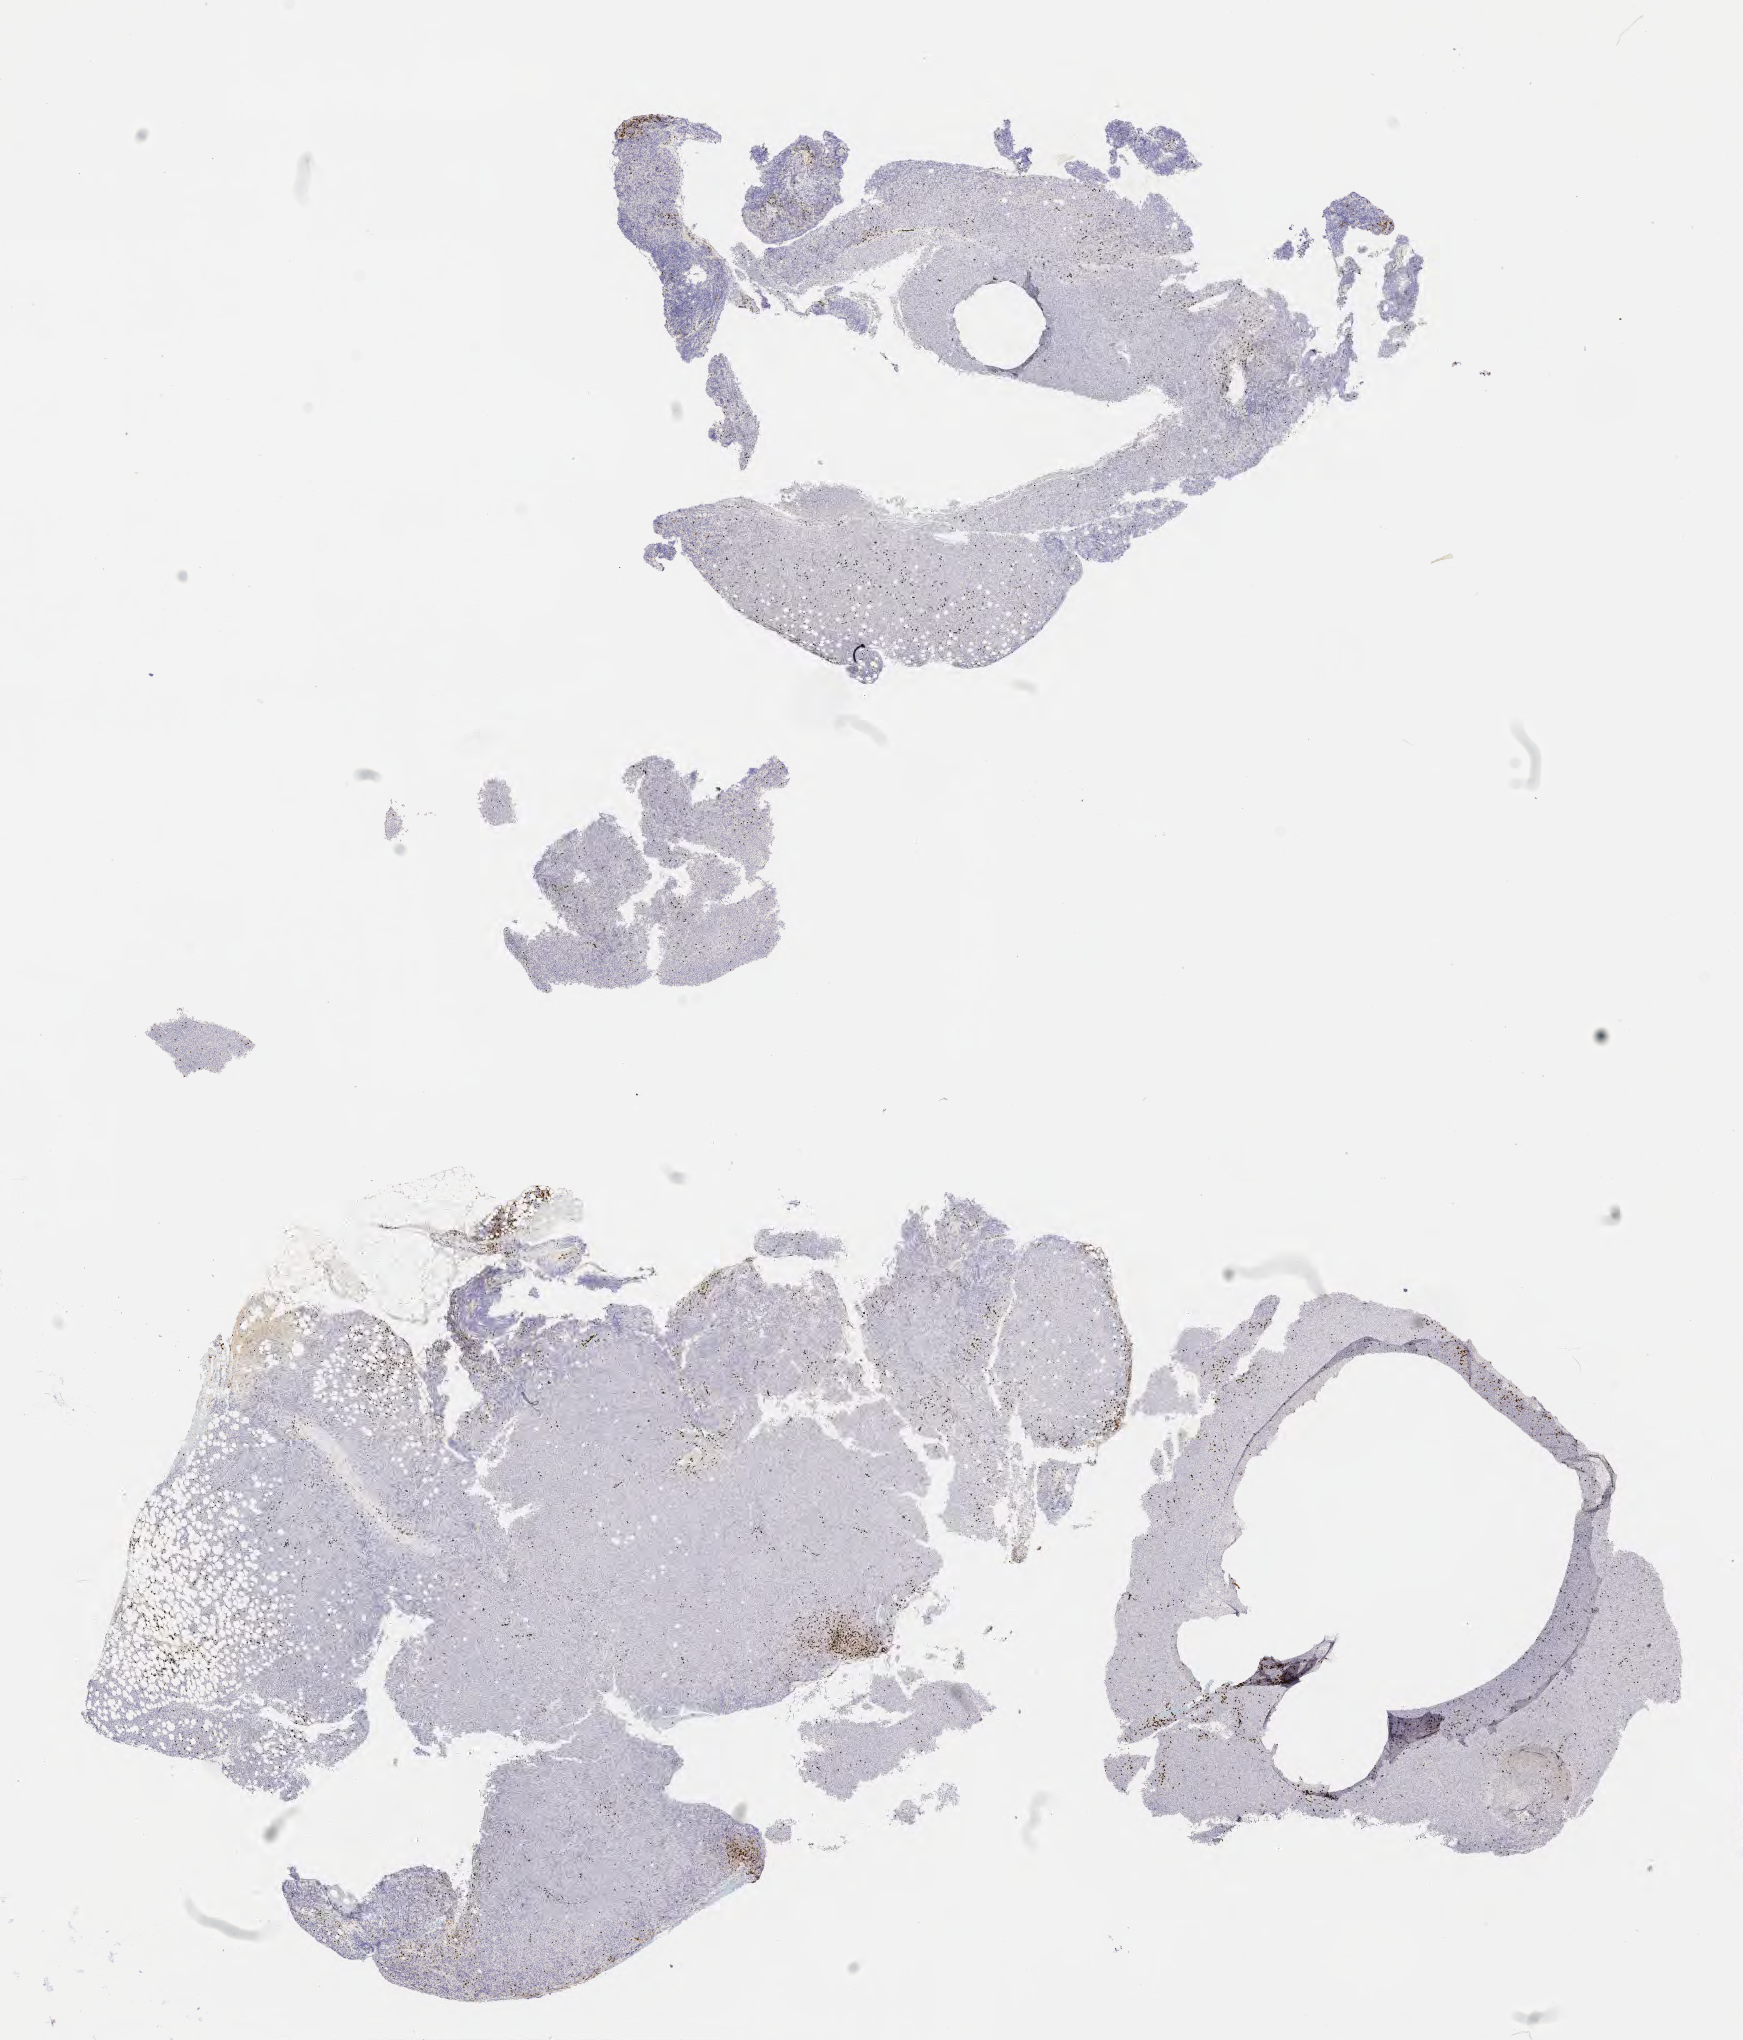
Immunohistochemistry (IHC) whole-slide image stained for CD3 — whole scanned area (about 14.1 x 16.5 mm) shown as a low-resolution overview, tumor tissue. Patient female; 32 years old.
Histologic diagnosis: Diffuse large B-cell lymphoma, NOS.